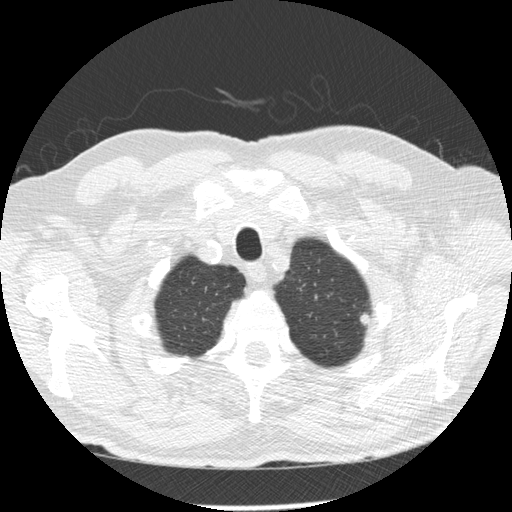
Low-dose screening chest CT, axial slice. Third annual screen. Lung window (W 1500 / L -600 HU). Slice 23 of 258 in the series. 512 × 512 image matrix. Male participant, aged 73 years at enrolment.
• Expert-annotated lung lesion, box from (x=349, y=297) to (x=389, y=336) px.
• The exam's reader record, not a measurement of the box and not confirmed to be the same lesion: non-calcified nodule or mass ≥4 mm, left upper lobe, 8 × 7 mm, poorly defined margins, mixed attenuation, pre-existing on the prior screen: no.
• Participant outcome: lung cancer diagnosed 93 days after this screen — adenocarcinoma, NOS, left upper lobe, poorly differentiated (G3), stage IB (AJCC 6th edition), 10 mm at pathology.